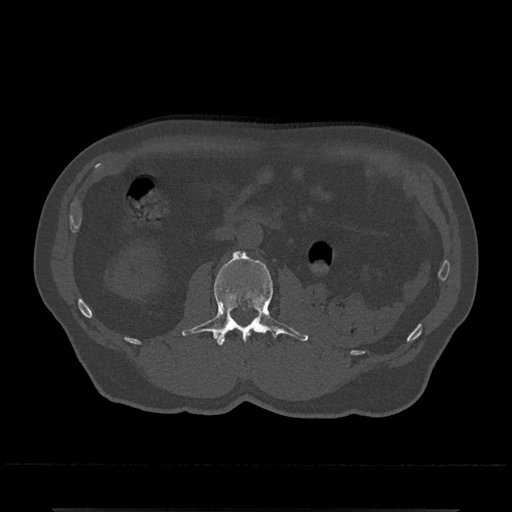
CT including the spine, one axial slice; slice 295 of 797 in the series (ordered by position); reconstruction kernel Br40s/3; 120 kVp; bone window (W 1800 / L 400 HU); 0.5 mm slice thickness; 512 × 512 image matrix. Patient: male, 67 years. Case-level facts recorded for this patient, not image findings: primary cancer: prostate.
Annotated regions visible in this slice (semi-automatically segmented with operator editing):
- L2 vertebra: bounding box <181,251,309,345> (left, top, right, bottom; pixels)